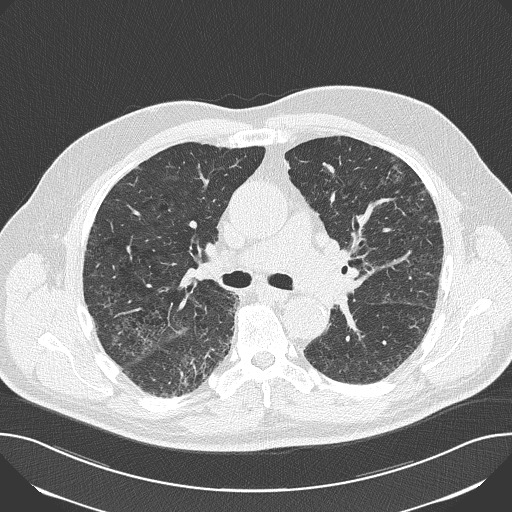
Axial slice from a low-dose chest CT screening exam. First (baseline) screen. Lung window (W 1500 / L -600 HU). Lung (sharp) reconstruction kernel (B50f). Slice 69 of 163 in the series. 512 × 512 image matrix. Male participant, aged 69 years at enrolment.
• Expert reader's lesion annotation, bounding box <165,356,207,399> (left, top, right, bottom; pixels).
• Screening reader's record for this exam: no non-calcified nodule ≥4 mm recorded.
• Official screen result: negative screen, significant abnormalities not suspicious for lung cancer.
• Participant outcome: lung cancer diagnosed 658 days after this screen — squamous cell carcinoma, NOS, right lower lobe, moderately differentiated (G2), stage IA (AJCC 6th edition), 25 mm at pathology.